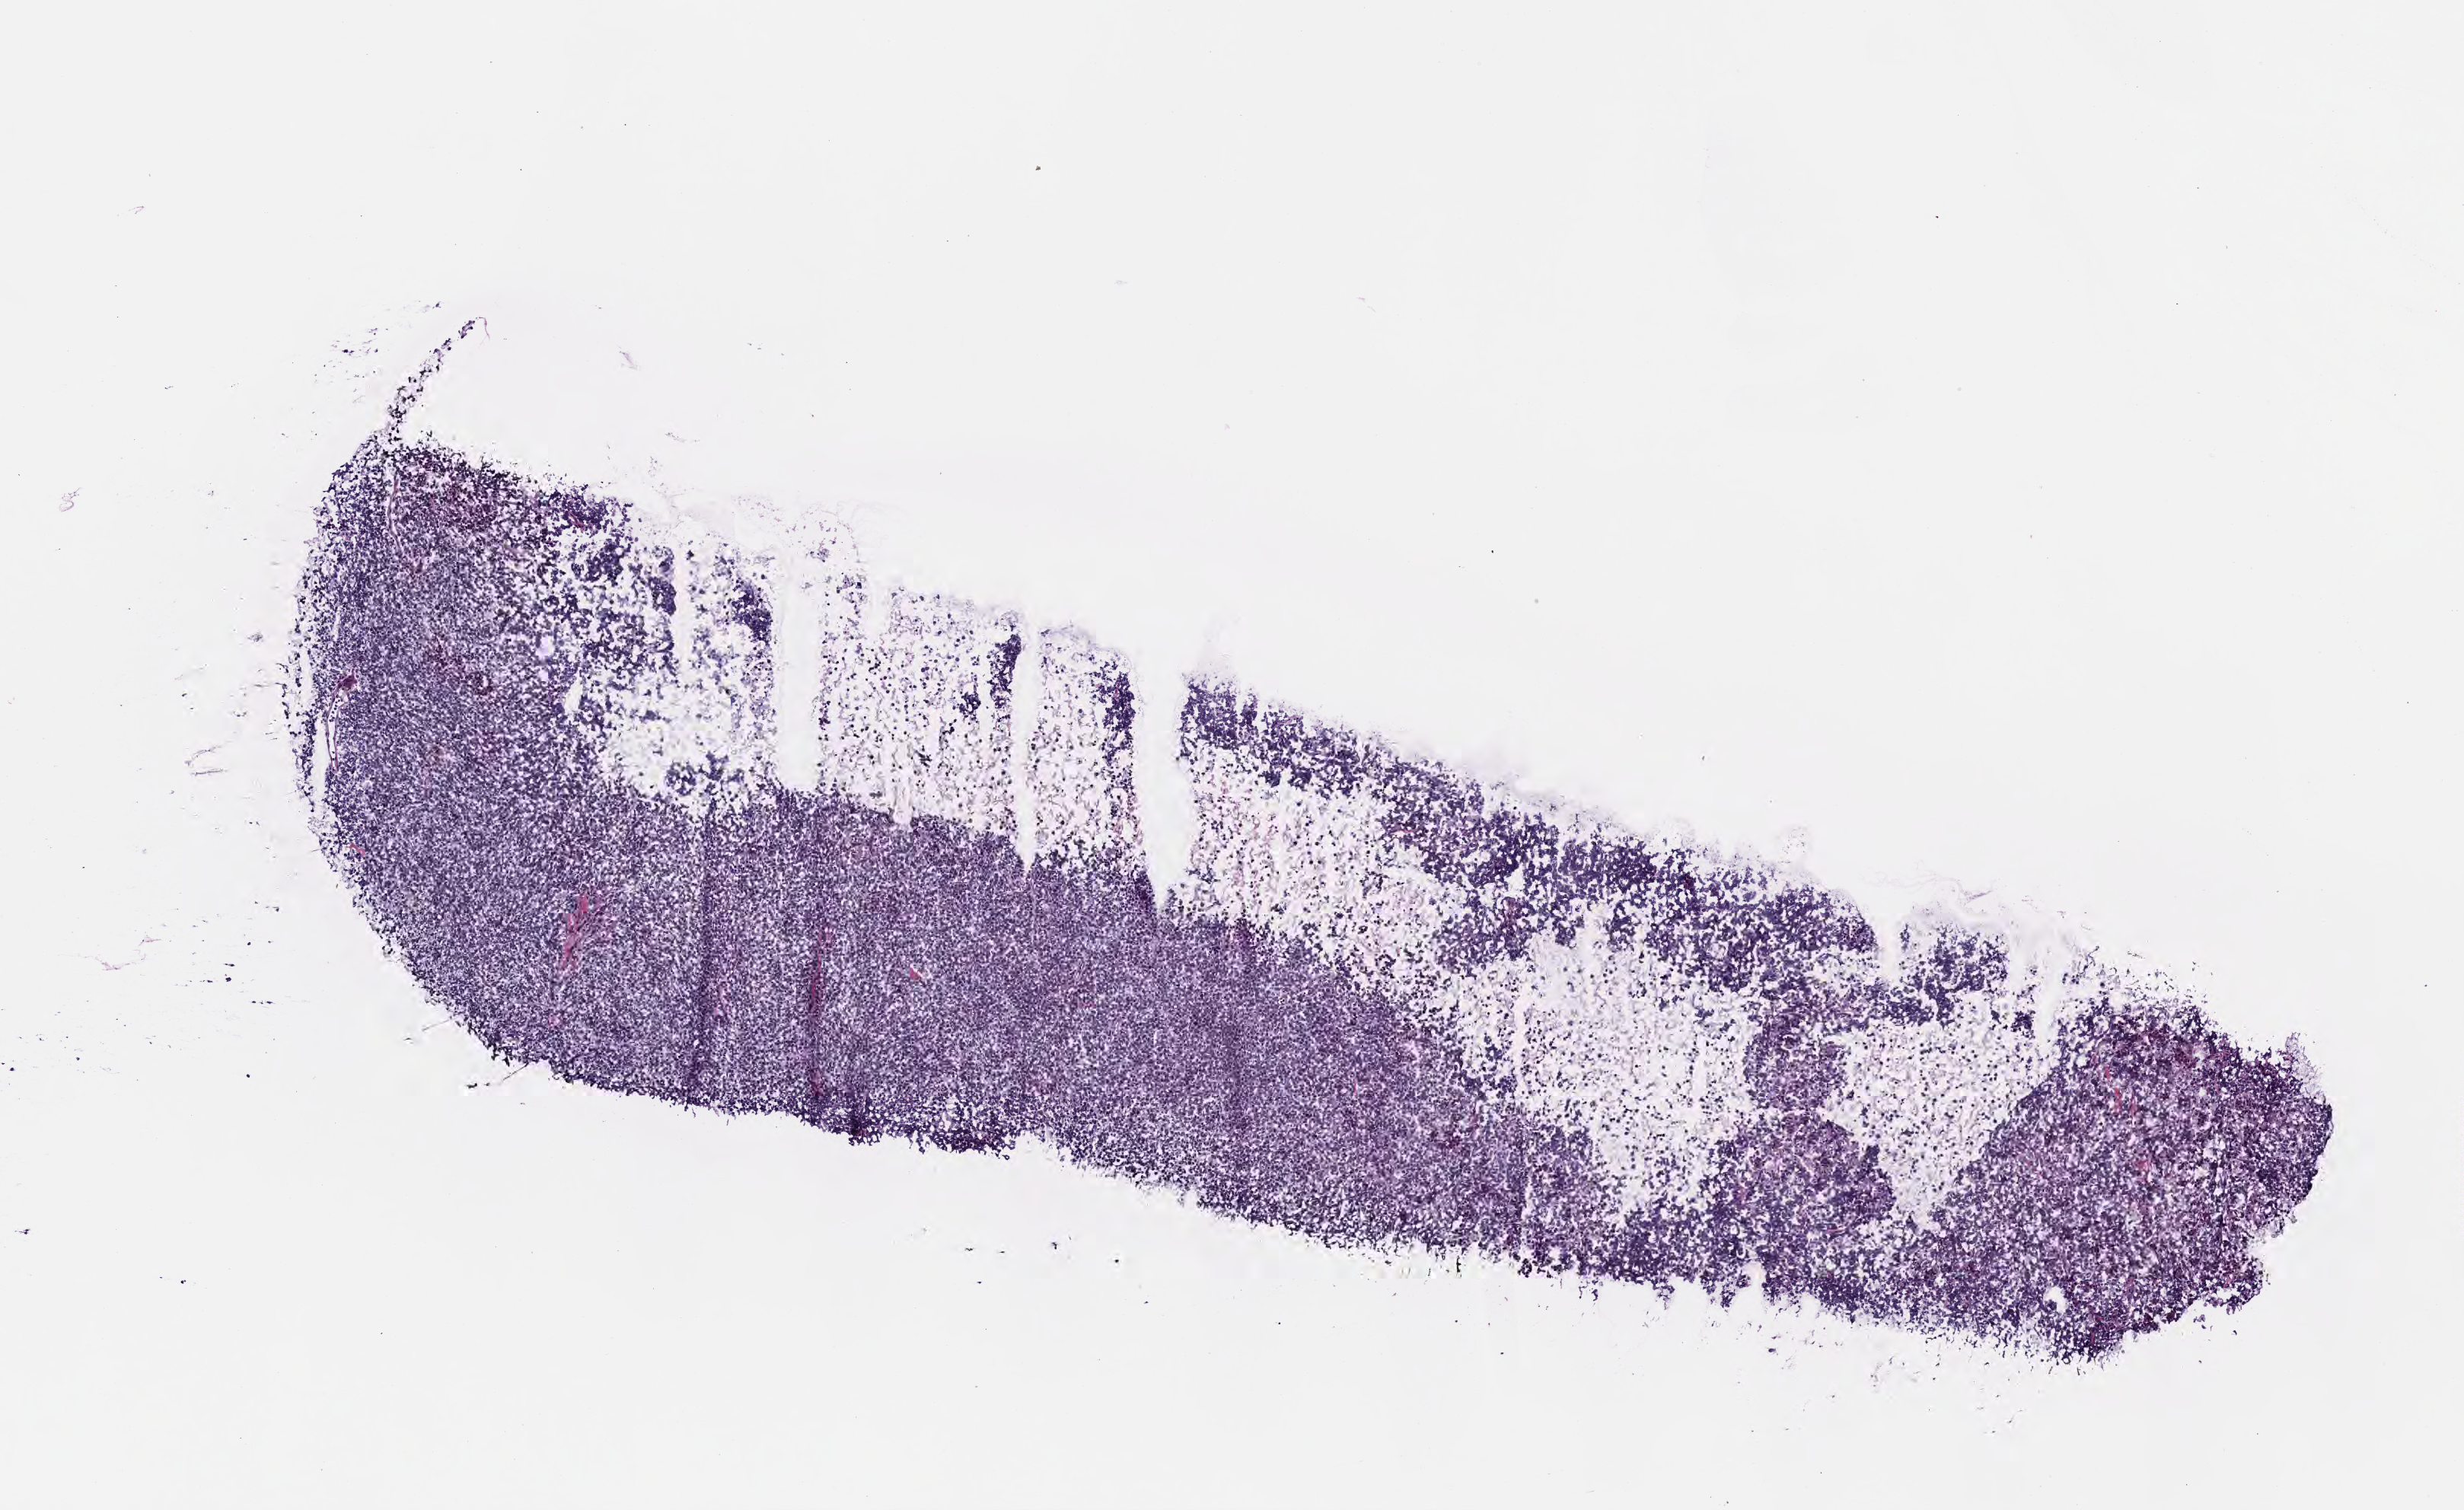
Whole-slide image, H&E stain — low-resolution overview of the scanned area, about 6.5 x 4.0 mm. Frozen section (tissue freezing medium). Primary tumor. Site: cranium. Female patient; age at initial diagnosis 7 years.
Histologic diagnosis: Burkitt lymphoma, NOS.